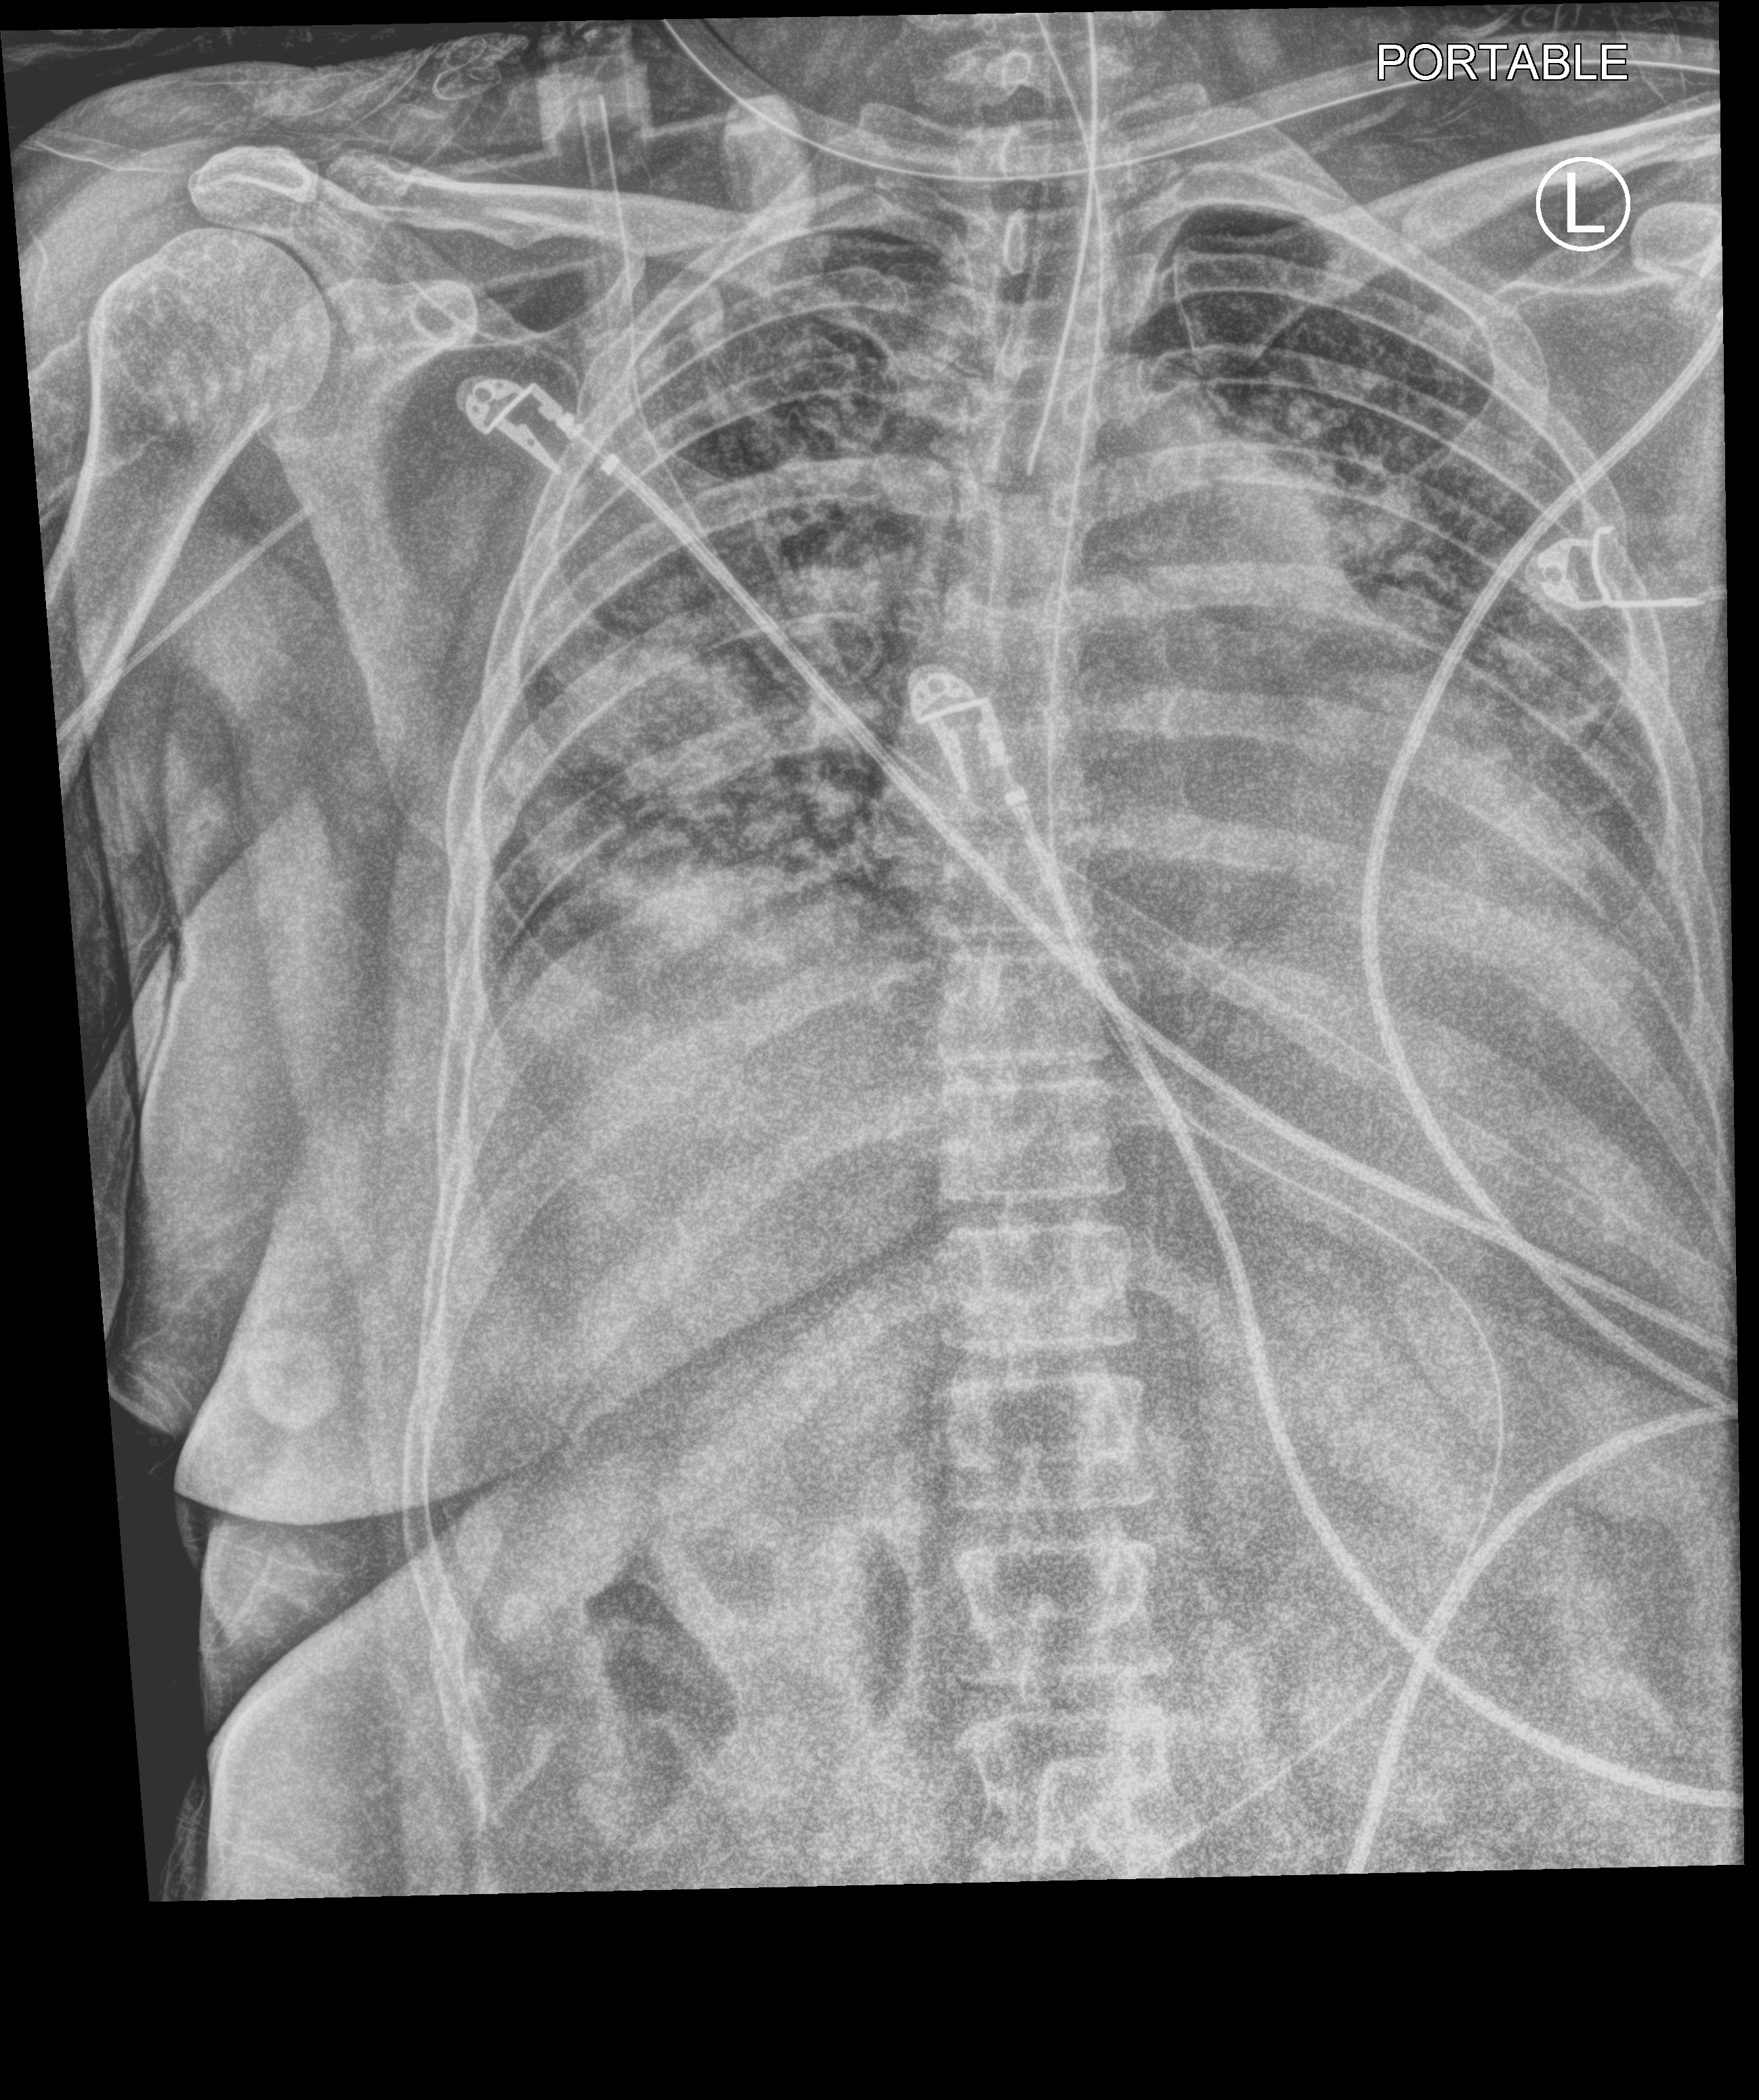
Bedside chest radiograph (computed radiography); anteroposterior (AP) projection. Female patient hospitalised with COVID-19, age 18–59 years.
Hospital-stay facts (about this admission, not read from this image; timing relative to this image not recorded):
- other chronic lung disease (admission record): no
- mechanically ventilated during this hospital stay: yes